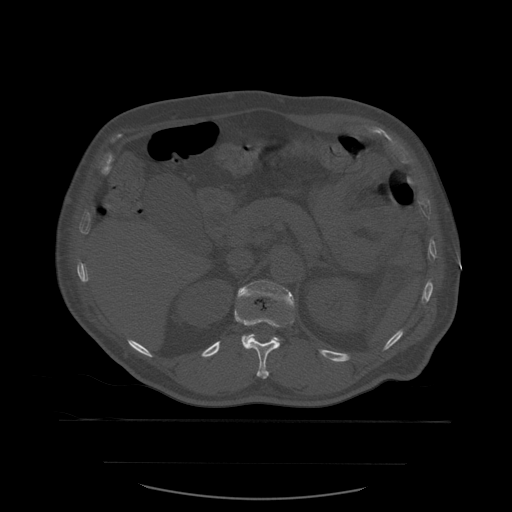
CT including the spine, one axial slice; slice 263 of 590 in the series (ordered by position); bone window (W 1800 / L 400 HU); 512 × 512 image matrix. Patient age 71 years. From the clinical record (not read from this slice): primary cancer: lung; vertebrae with lytic lesions (as recorded): T1, T2, L5, S1.
Outlined on this slice (semi-automatically segmented with operator editing):
- L1 vertebra: bounding box (x1, y1, x2, y2) in pixels: (235, 281, 295, 342)
- T12 vertebra: (235, 310, 294, 379)